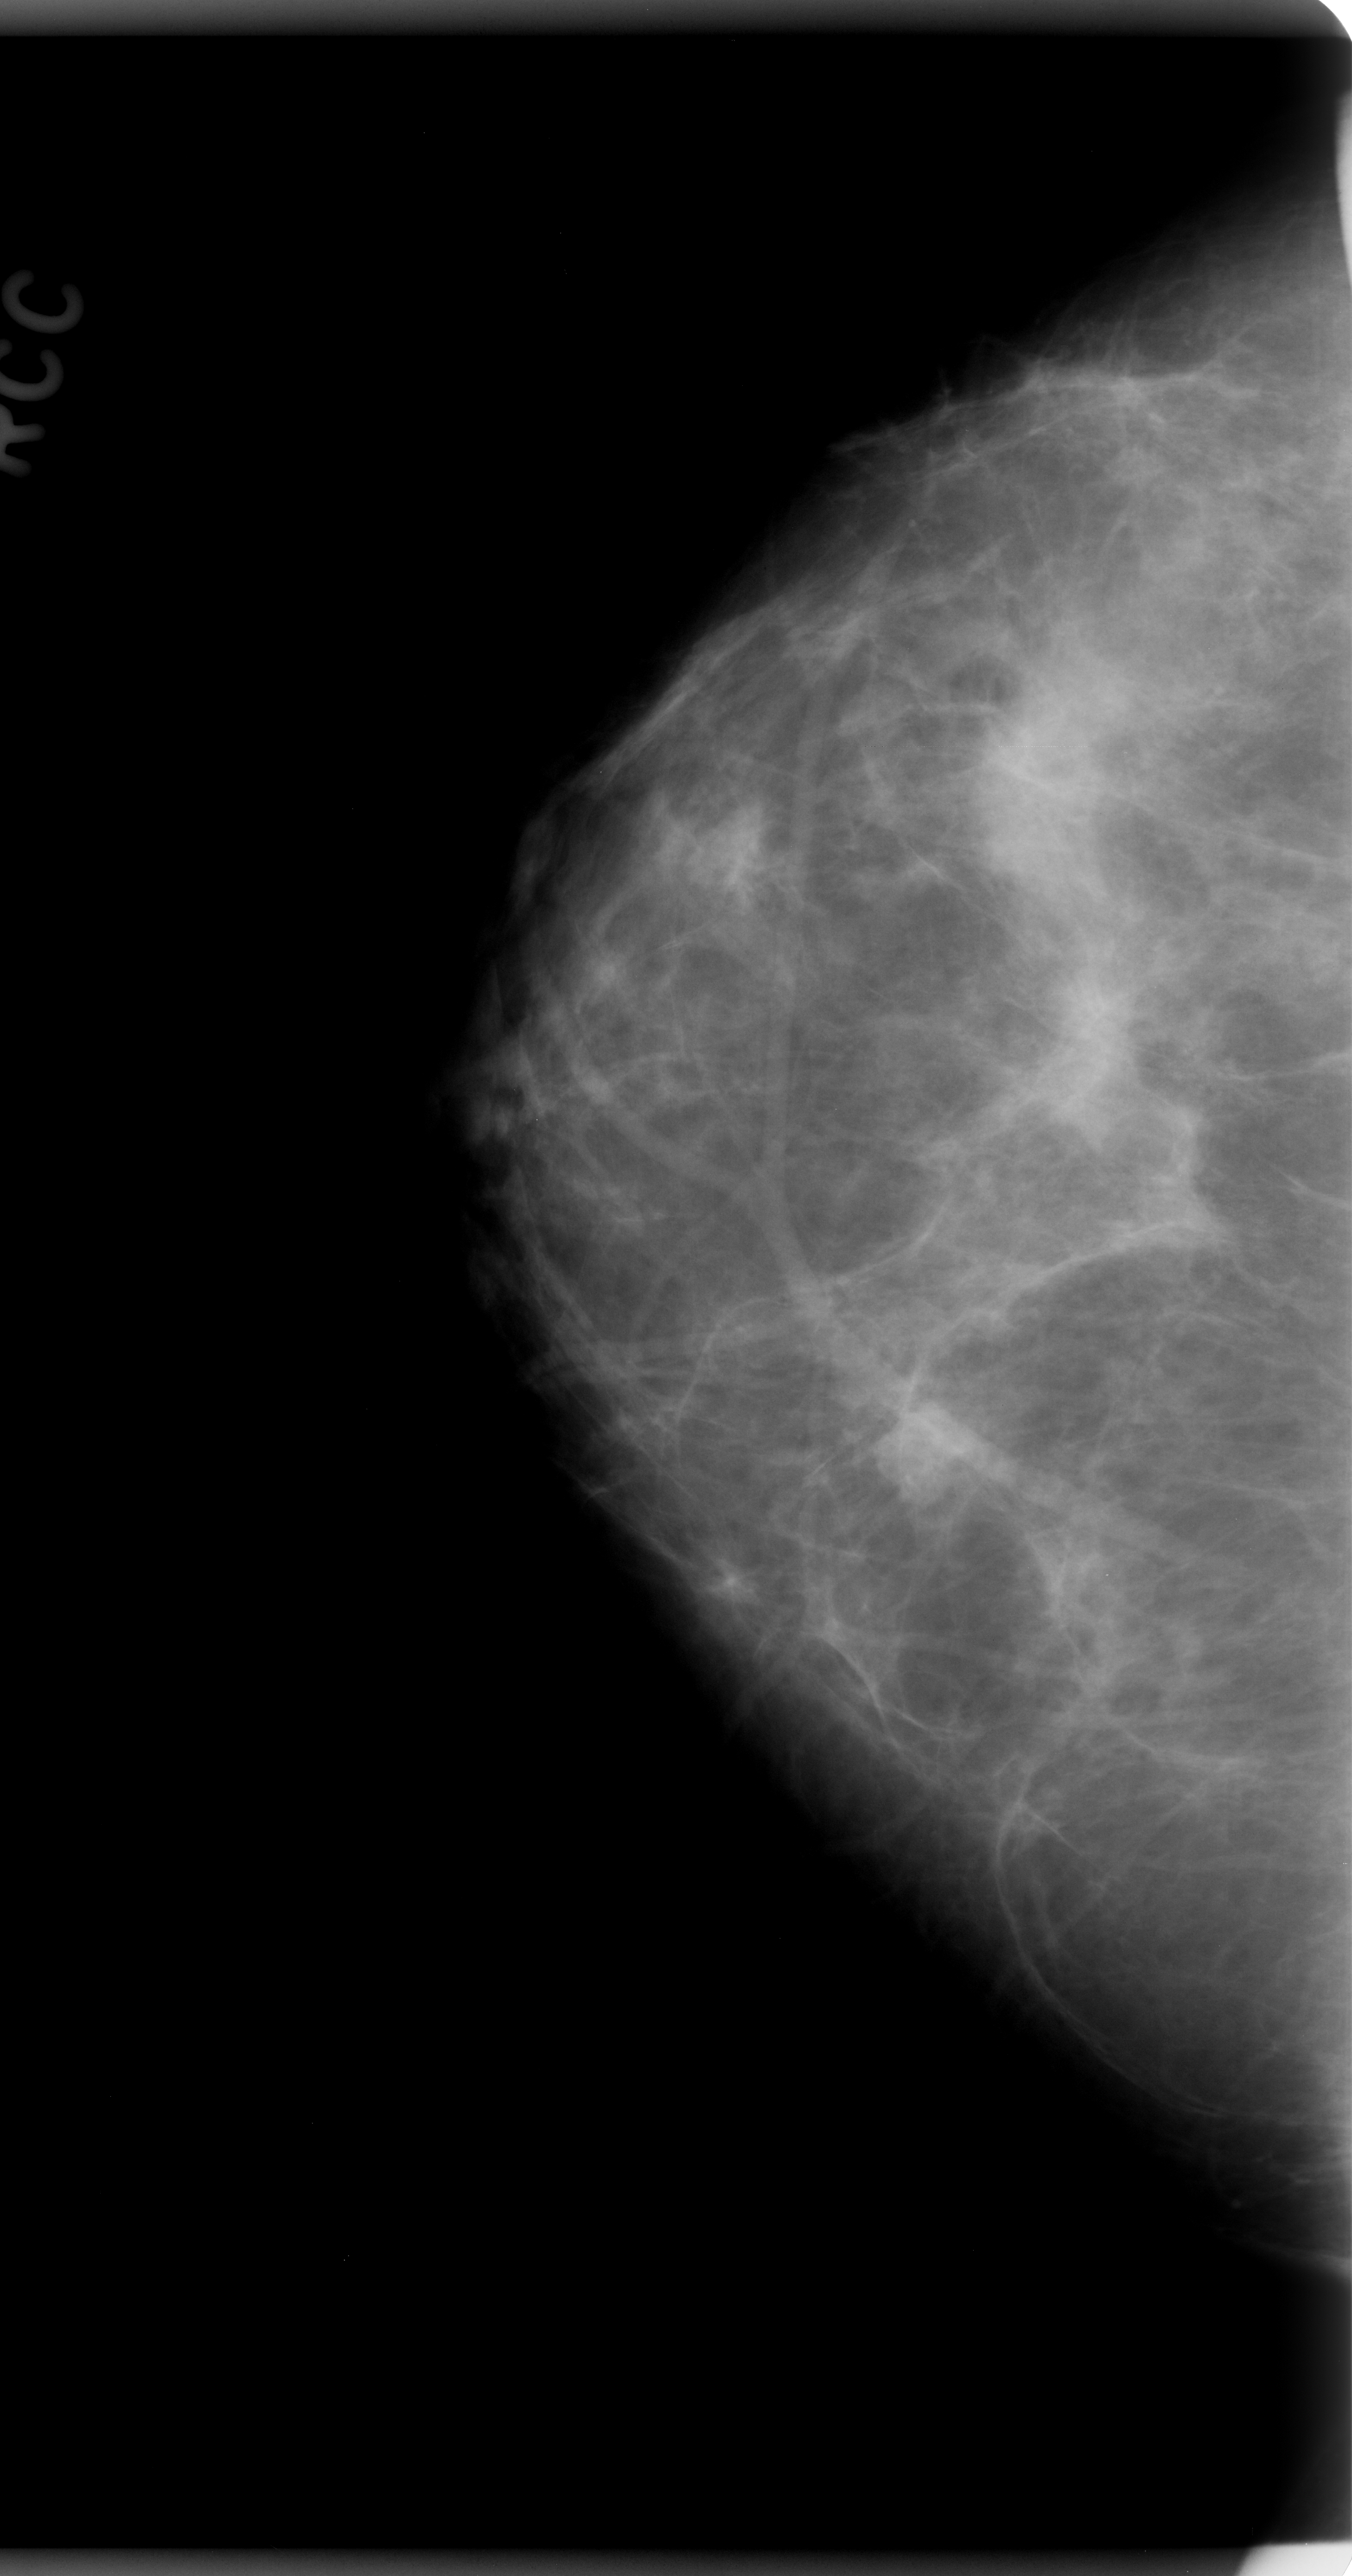
Digitized screen-film mammogram, right breast, CC view, breast composition: scattered fibroglandular densities (BI-RADS density category 2 of 4).
Finding: mass, shape oval, margins microlobulated; BI-RADS assessment category 4; subtlety rating 5 on a 1 (subtle) to 5 (obvious) scale; pathology result (as recorded, not read from the image): benign.